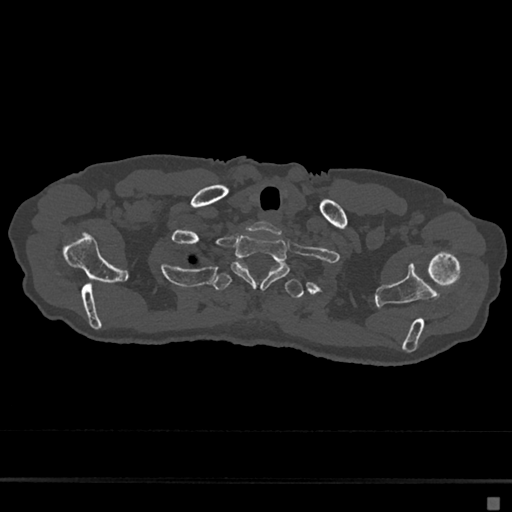
CT including the spine, one axial slice; slice 601 of 797 in the series (ordered by position); 120 kVp; bone window (W 1800 / L 400 HU); 0.5 mm slice thickness; 512 × 512 image matrix. Patient: female, 68 years. From the clinical record (not read from this slice): primary cancer: renal.
Structures marked on this image (semi-automatic segmentation, software-assisted and operator-edited):
- T1 vertebra: bounding box [x1, y1, x2, y2] px = [231, 235, 290, 290]
- T2 vertebra: [212, 267, 304, 299]